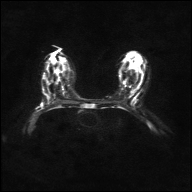
Breast MRI, one axial slice. Slice 19 of 36 in the series (ordered by position). Diffusion-weighted series; image 2 of 4 stored at this slice position (different b-values; order by instance number). 1.5 T. 4 mm slice thickness. 192 × 192 image matrix. Female patient.
Outlined on this slice (expert manual segmentation):
- tumour on diffusion-weighted imaging: bounding box (x1, y1, x2, y2) in pixels: (41, 104, 44, 107)